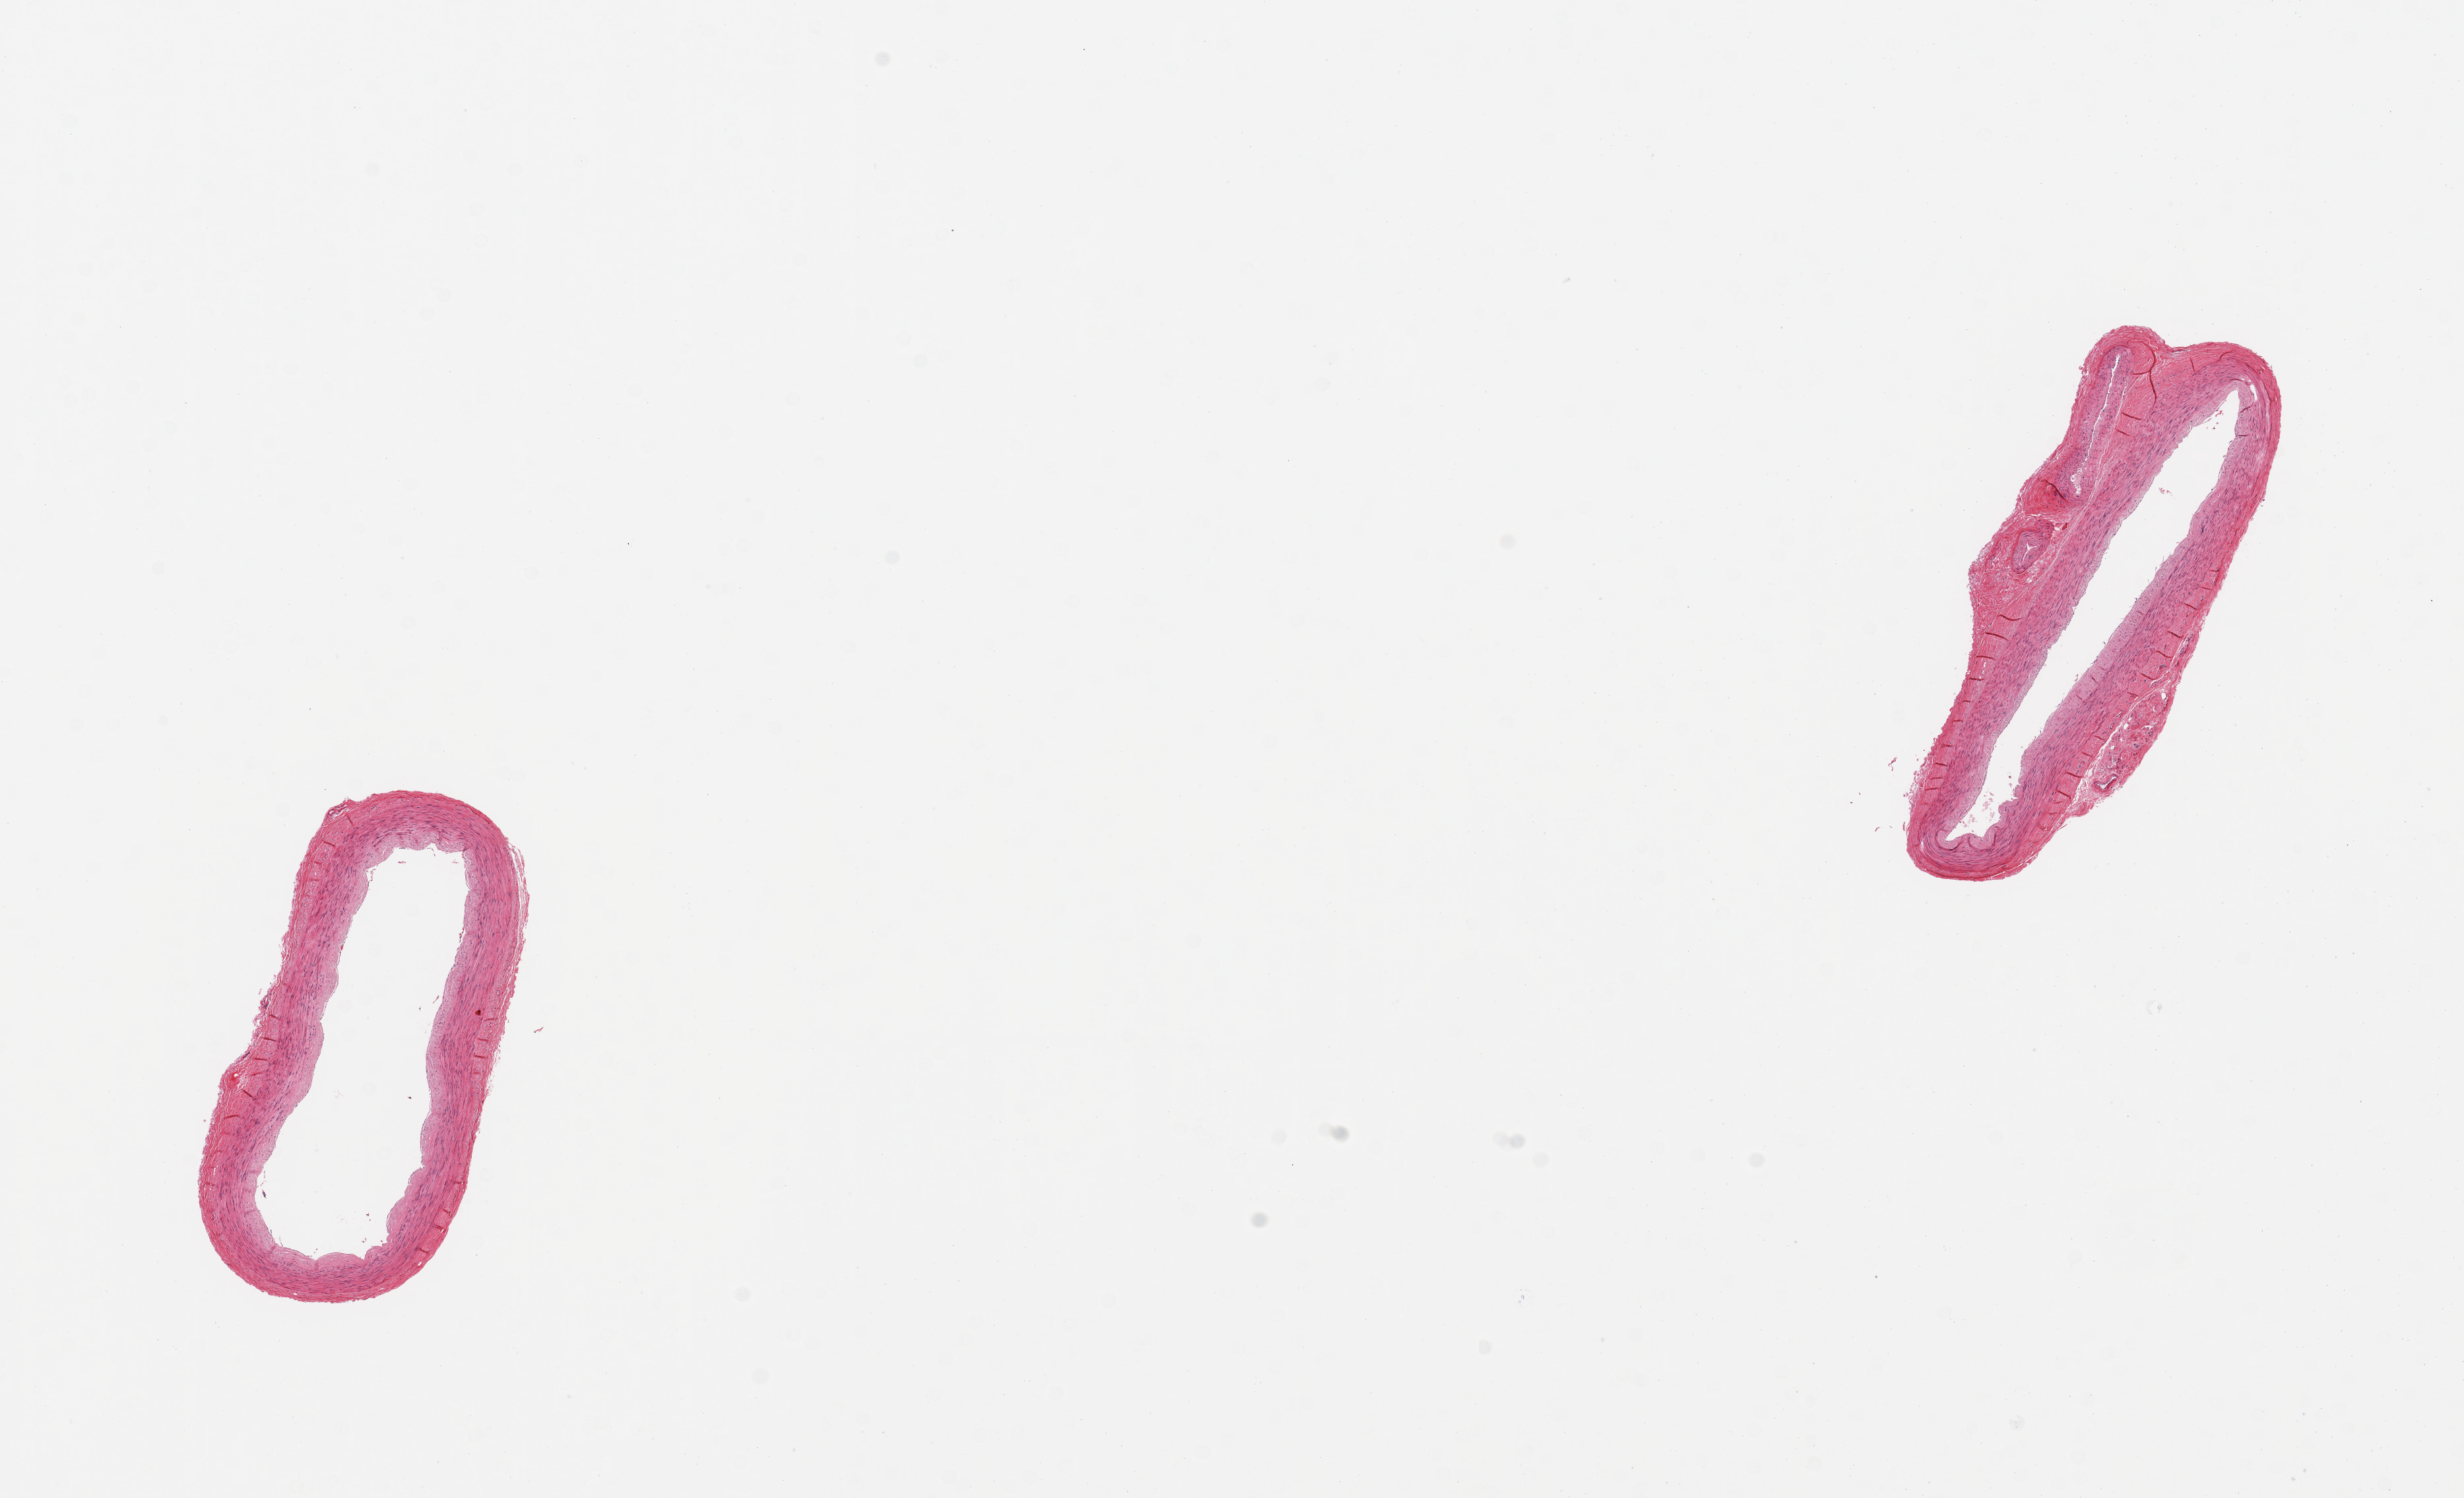
Whole-slide image, haematoxylin and eosin stain, brightfield, whole scanned area (about 14.8 x 9.0 mm) shown as a low-resolution overview; PAXgene-fixed, paraffin-embedded tissue; section of tibial artery (target tissue); tissue donor sample. Donor: female.
Reviewer comment on this tissue sample: 2 pieces; mild plaque.